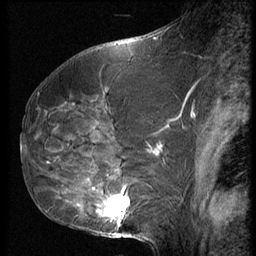
Breast MRI (dynamic contrast-enhanced), one sagittal slice; slice 30 of 62 in the series (ordered by position); 3 images stored at this slice position (order not interpretable as contrast timing); 1.5 T; TE 4.2 ms, TR 9 ms; 2.5 mm slice thickness; 256 × 256 image matrix, field of view 180 × 180 mm. Patient: female, 50 years. Case-level facts recorded for this patient, not image findings: setting: breast cancer imaged before/during neoadjuvant chemotherapy; receptor status: HR-positive, HER2-negative.
Outlined on this slice (semi-automatic segmentation, software-assisted and operator-edited):
- analysis volume of interest (the breast-tissue region the enhancement analysis was run in; not a lesion): bounding box [x1, y1, x2, y2] px = [59, 125, 139, 238]
- tumour enhancement mask (voxels above the 140 % enhancement threshold inside the analysis volume of interest): [105, 194, 130, 222]